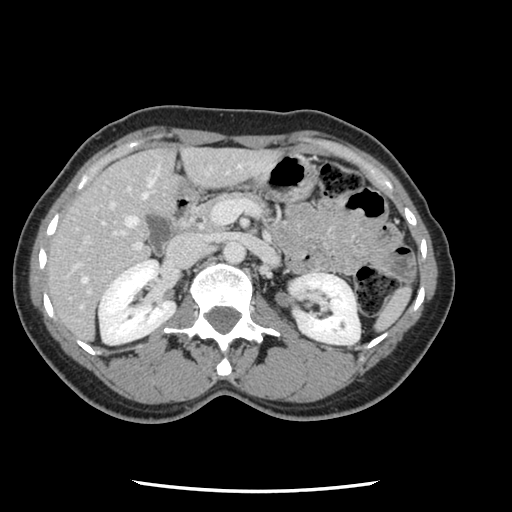
Contrast-enhanced abdominal CT, one axial slice. Slice 55 of 134 in the series (ordered by position). Intravenous contrast given. Soft-tissue window (W 400 / L 40 HU). 512 × 512 image matrix. Female patient, age 43 years. From the clinical record (not read from this slice): diagnosis: colorectal cancer liver metastases, imaged before liver resection; multiple liver metastases: yes; largest metastasis: 3.4 cm; disease in both lobes: yes.
Annotated regions visible in this slice (outlined manually by an expert reader):
- hepatic veins: bounding box [x1, y1, x2, y2] px = [82, 169, 159, 284]
- liver: [47, 147, 277, 341]
- planned liver remnant (the part of the liver to remain after resection): [47, 148, 178, 328]
- portal vein (with intrahepatic branches): [67, 164, 258, 295]